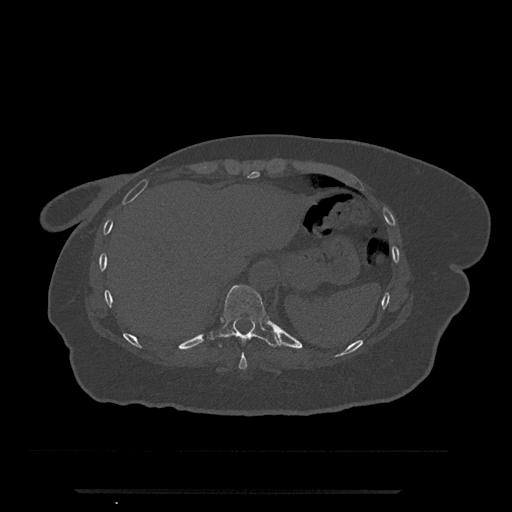
CT including the spine, one axial slice. Reconstruction kernel Br40s/3. 120 kVp. Bone window (W 1800 / L 400 HU). 512 × 512 image matrix, field of view 440 × 440 mm. Patient: female, 51 years. From the clinical record (not read from this slice): primary cancer: neuro.
Annotated regions visible in this slice (semi-automatic segmentation, software-assisted and operator-edited):
- T10 vertebra: bounding box [x1, y1, x2, y2] px = [212, 285, 279, 347]
- T9 vertebra: [238, 352, 247, 370]